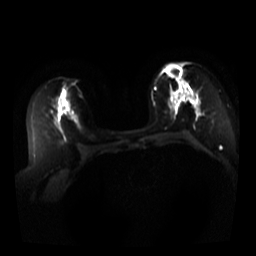
Breast MRI, one axial slice; slice 20 of 44 in the series (ordered by position); diffusion-weighted series; image 2 of 4 stored at this slice position (different b-values; order by instance number); 3 T; 5 mm slice thickness; 256 × 256 image matrix, field of view 340 × 340 mm. Female patient.
Annotated regions visible in this slice (expert manual segmentation):
- tumour on diffusion-weighted imaging: box from (x=166, y=63) to (x=192, y=99) px